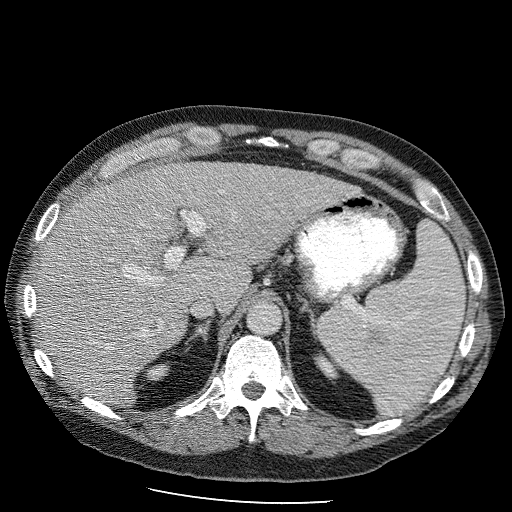
Contrast-enhanced abdominal CT (liver protocol), one axial slice. Position 69 of 98 along the scan axis. Reconstruction kernel STANDARD. Soft-tissue window (W 400 / L 40 HU). 2.5 mm slice thickness. 512 × 512 image matrix. From the clinical record (not read from this slice): diagnosis: hepatocellular carcinoma (patient treated with transarterial chemoembolisation; whether this scan precedes or follows treatment is not stated here); TNM stage (as recorded): Stage-II; Child-Pugh class: B; tumour differentiation: moderately differentiated; tumour nodularity: uninodular.
Annotated regions visible in this slice (semi-automatically segmented with operator editing):
- liver parenchyma outside the tumour (the mass and vessels are separate outlines, so this box may not span the whole liver): bounding box [x1, y1, x2, y2] px = [34, 162, 348, 408]
- liver vessels: [123, 220, 211, 336]